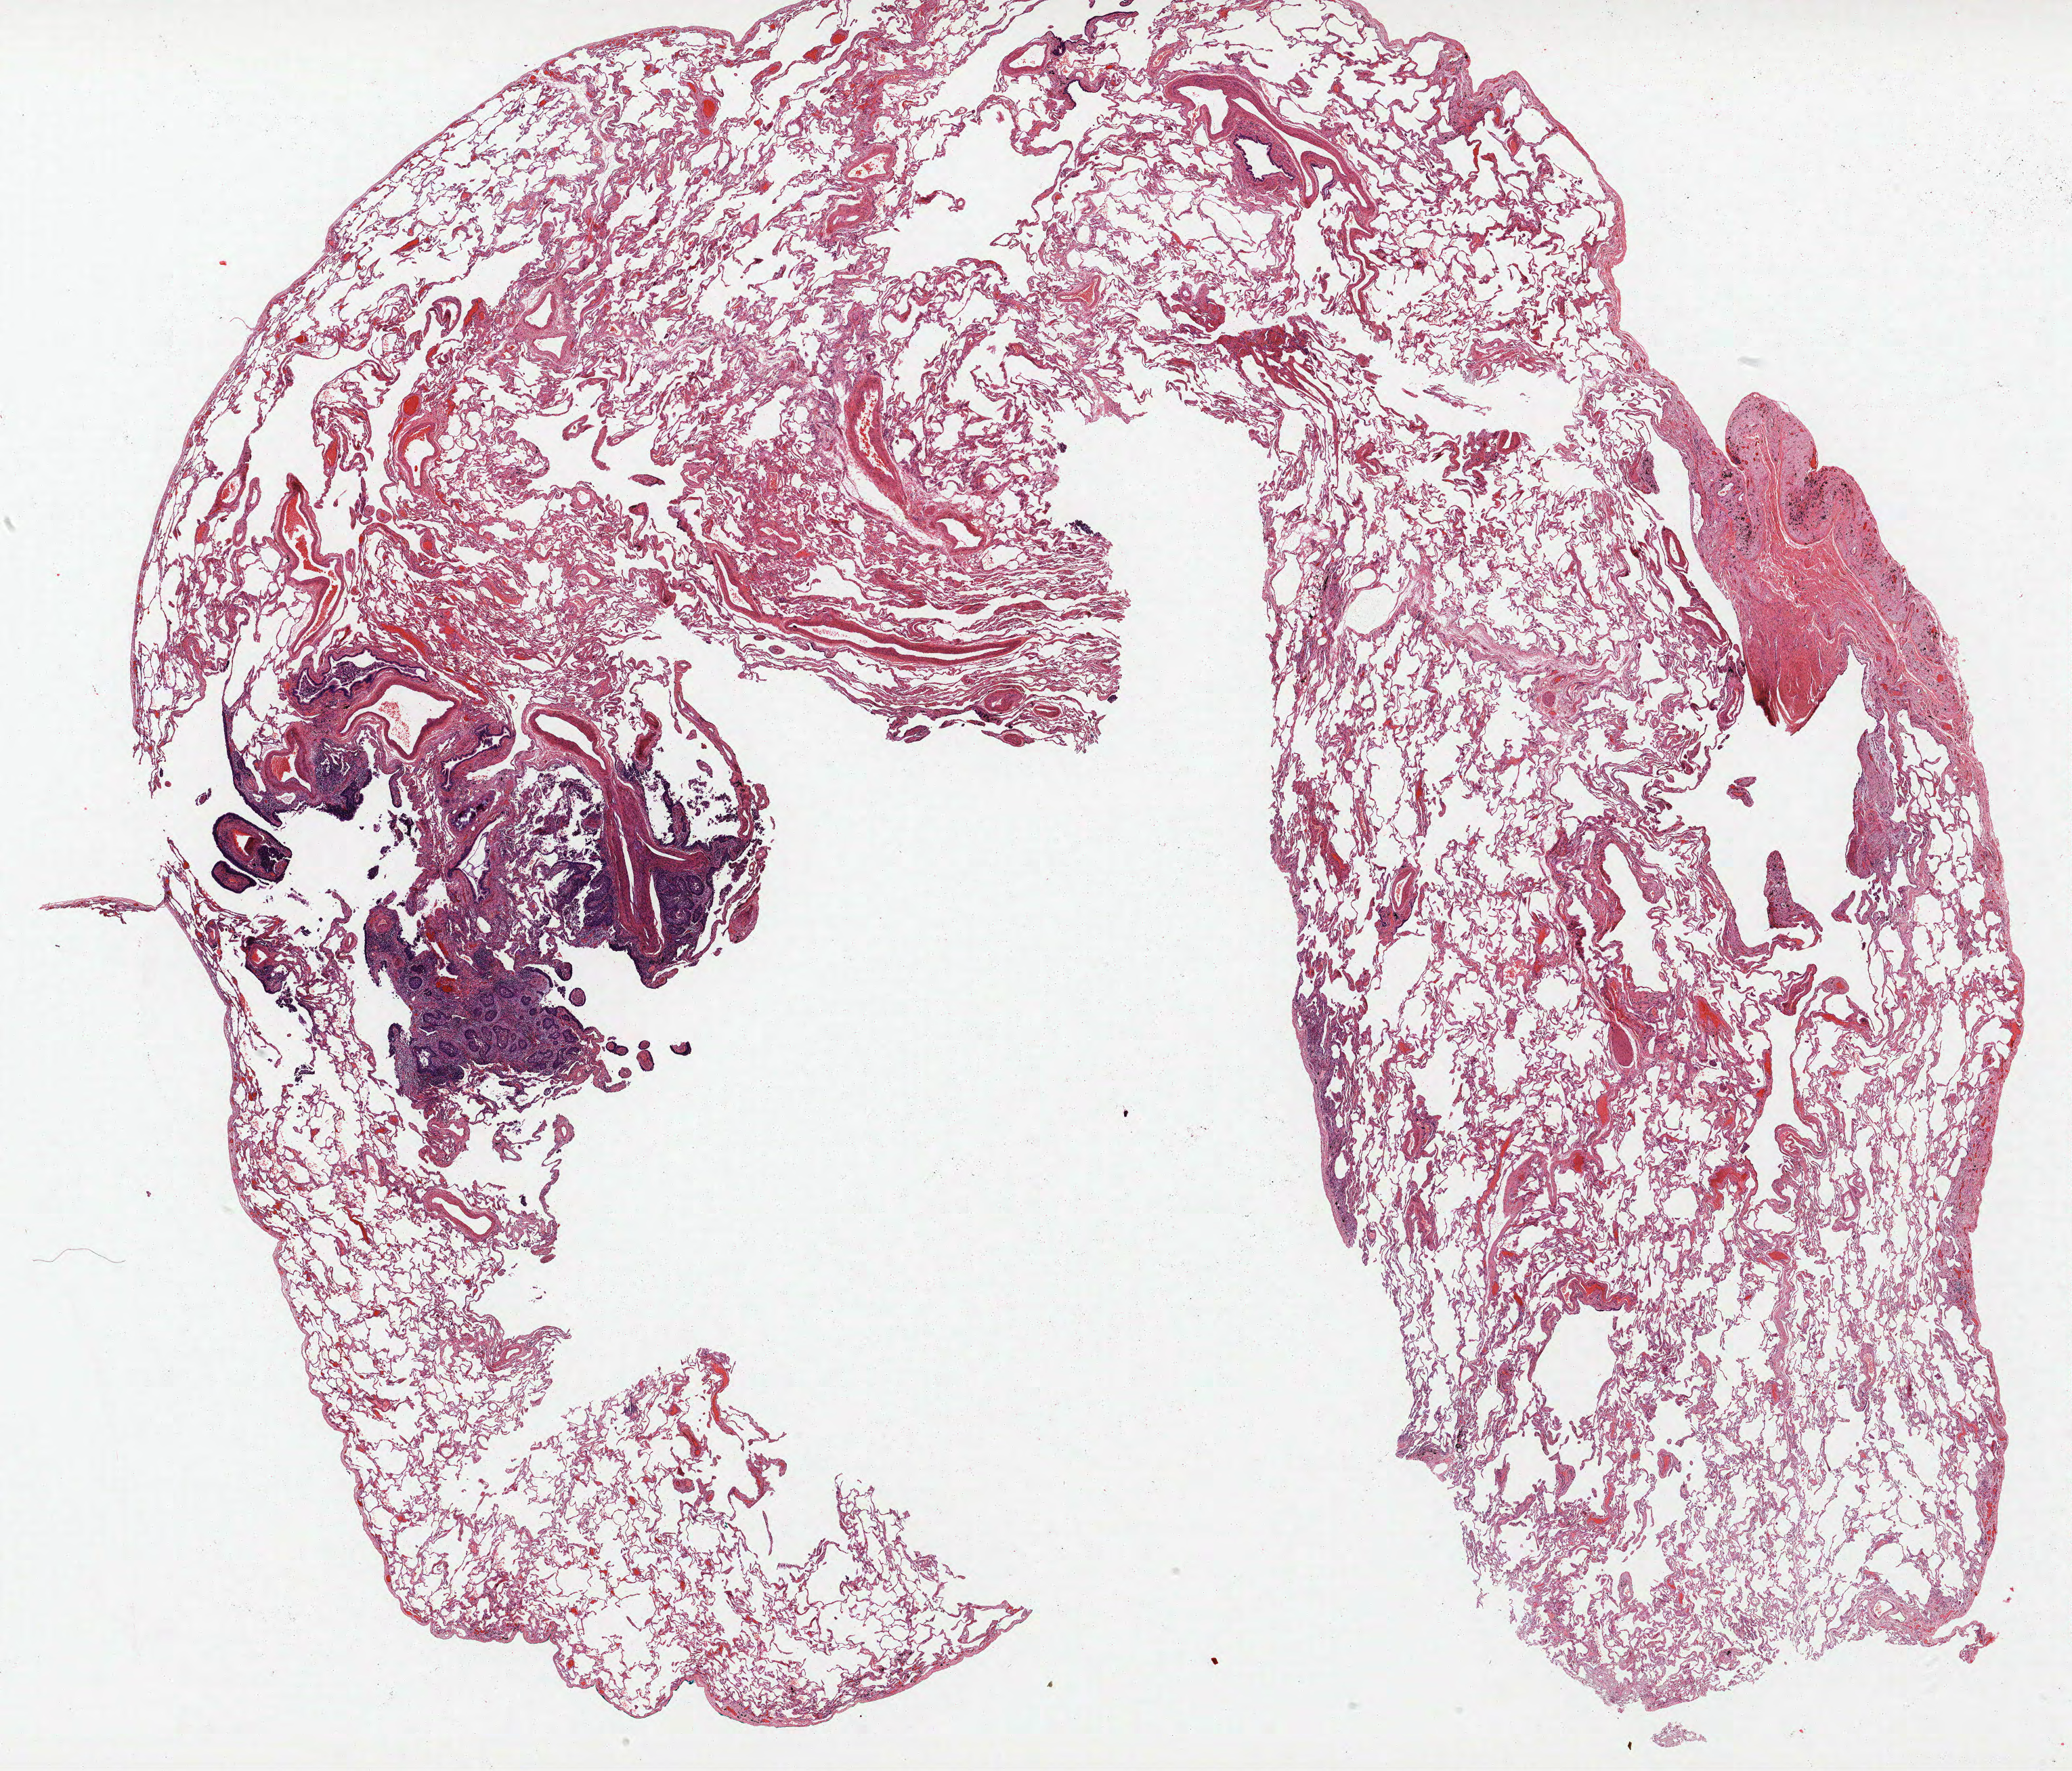
H&E-stained whole-slide image — a low-resolution overview of the entire scanned area, about 24.5 x 20.9 mm (from a 40x scan). FFPE section. Lung tissue. Female patient, aged 73 at enrolment. Former smoker at enrolment. Grade: moderately differentiated (G2).
Tumour size (pathology): 15 mm. Primary tumour location (clinical record): right upper lobe. Stage (AJCC 6th edition): IB. Participant's lung-cancer diagnosis: Adenocarcinoma, NOS (ICD-O-3 8140/3).